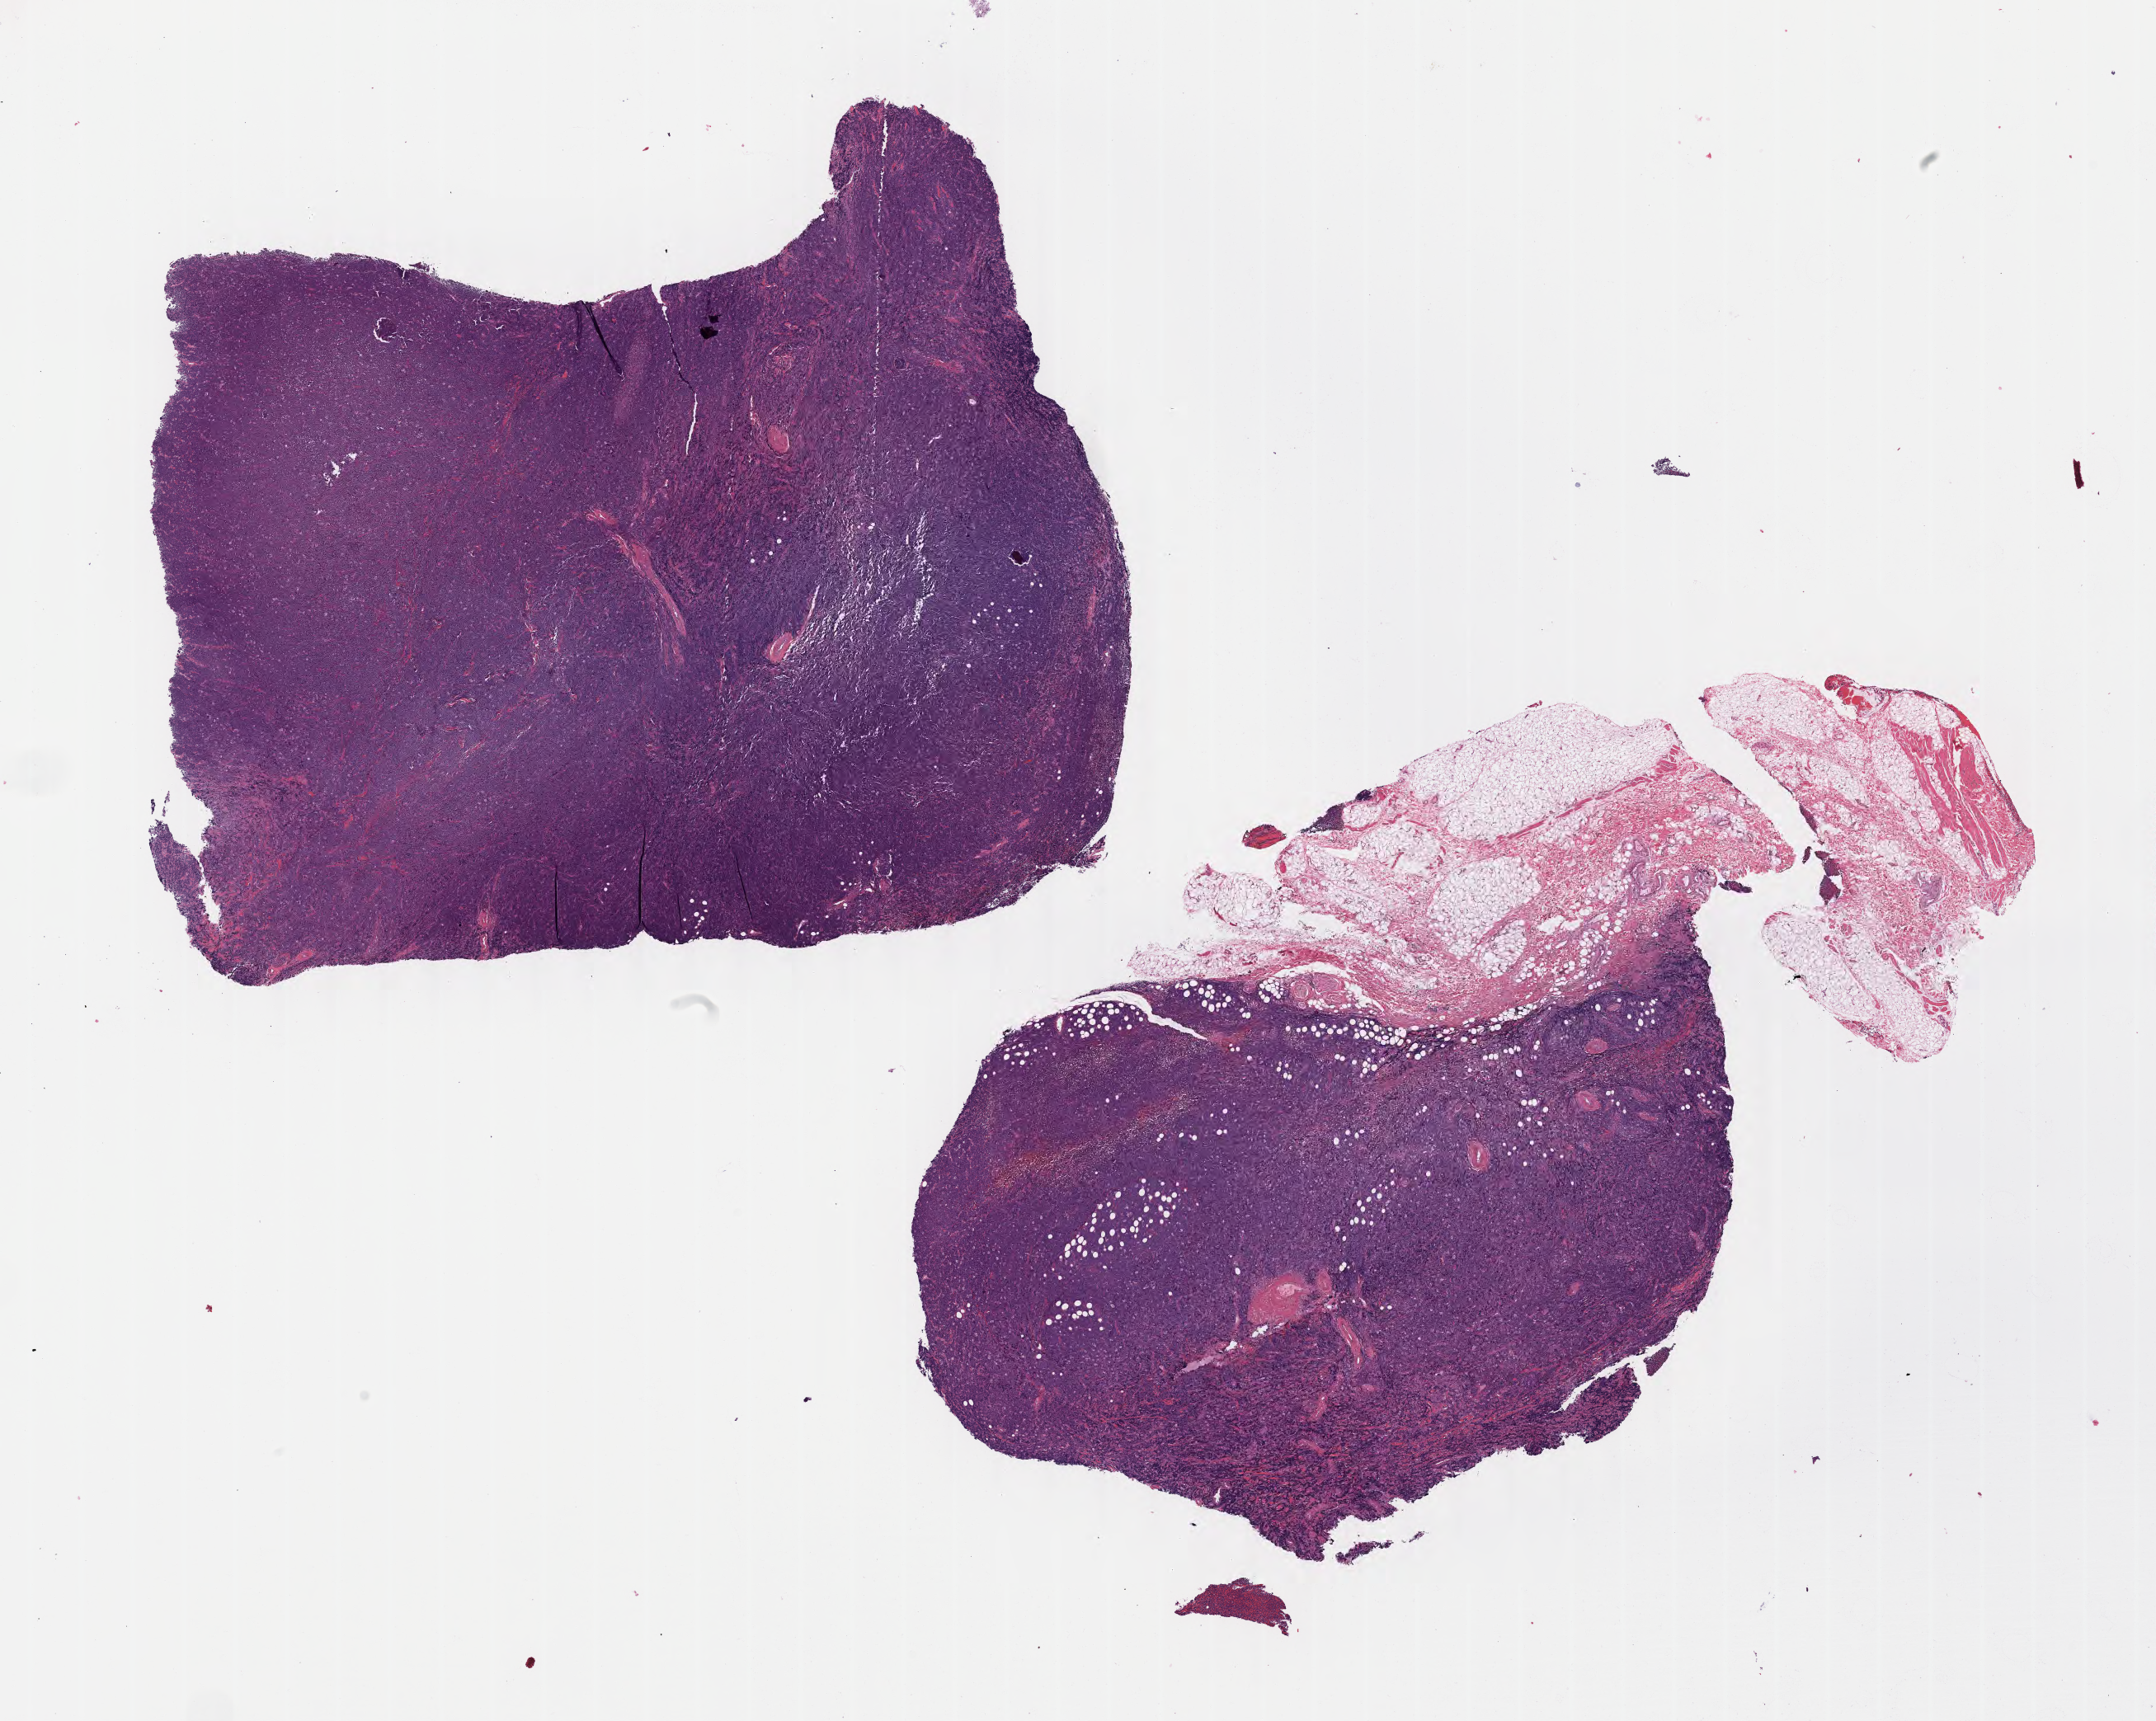
Whole-slide image, haematoxylin and eosin stain, shown as a low-resolution overview of the whole scanned area (about 21.1 x 16.9 mm); tumor tissue; site: cranium. Male patient; age at initial diagnosis 5 years.
- histologic diagnosis: Burkitt lymphoma, NOS